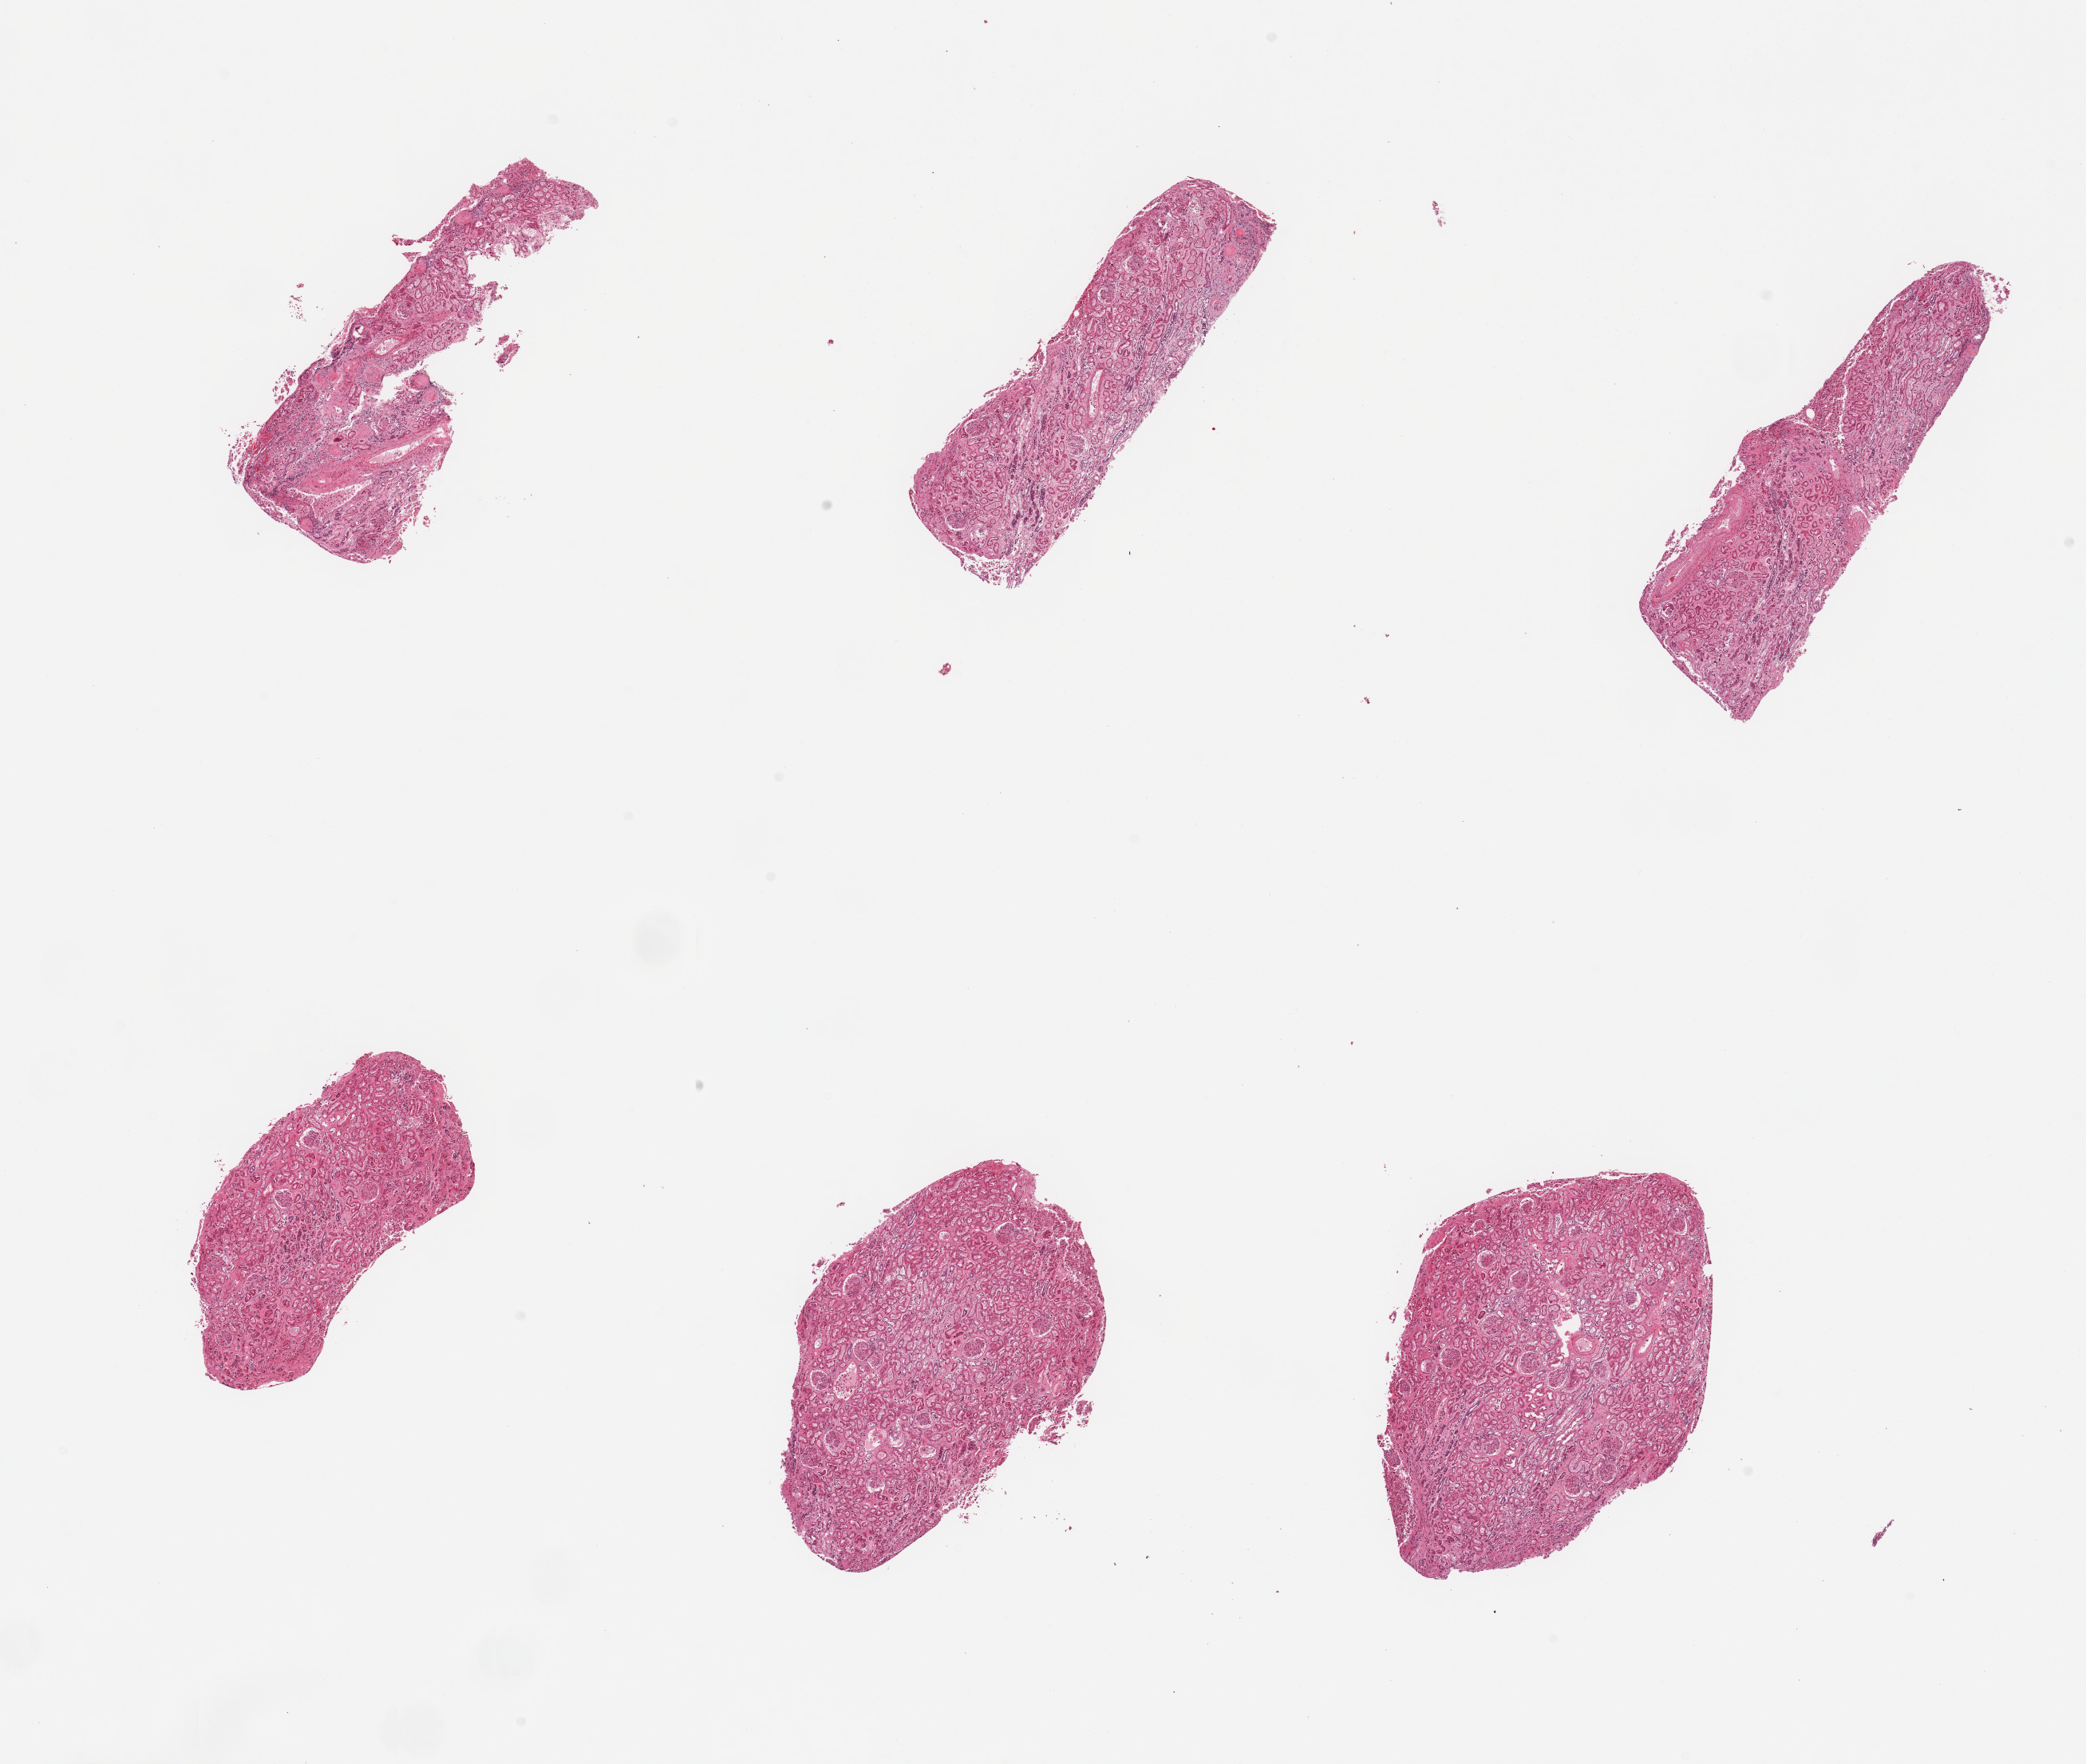
H&E whole-slide image, brightfield — low-resolution overview of the scanned area, about 20.7 x 17.5 mm (from a 20x scan); PAXgene-fixed, paraffin-embedded tissue; sampled site (target tissue): renal cortex; donor tissue sample. Donor sex: male.
- reviewer comment on this tissue sample: 6 pieces, glomeruli present, tubules moderately autolysis